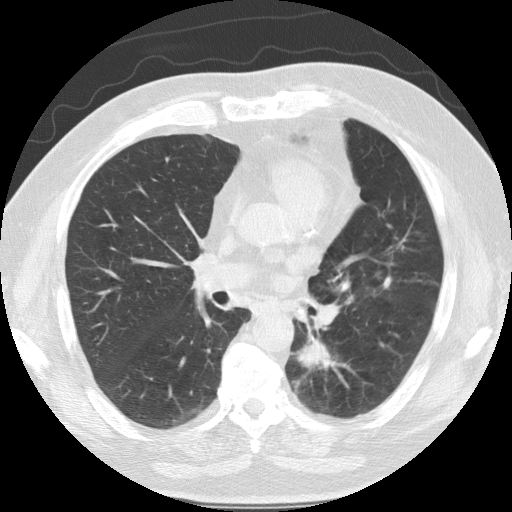
Chest CT (low-dose screening protocol), one axial image; baseline screening round; lung window (W 1500 / L -600 HU); 2.5 mm slice thickness; standard (soft-tissue) reconstruction kernel (STANDARD); slice 60 of 124 in the series; 512 × 512 image matrix, field of view 360 × 360 mm. Male participant, aged 68 years at enrolment.
Lesion marked by an expert reader, bounding box [x1, y1, x2, y2] px = [278, 316, 352, 396]. The screening reader recorded 3 non-calcified nodules or masses ≥4 mm on this exam (left lower lobe, lingula, right lower lobe); which of them this box marks is not recorded. Official screen result: positive, change unspecified: nodule(s) >= 4 mm or enlarging nodule(s), mass(es), or other non-specific abnormalities suspicious for lung cancer.